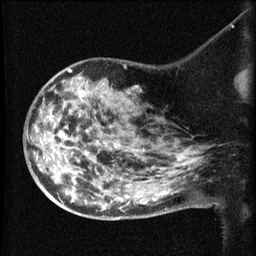
Breast MRI (dynamic contrast-enhanced), one sagittal slice; slice 40 of 60 in the series (ordered by position); dynamic contrast-enhanced series, image 2 of 3 at this slice position (ordered by acquisition); 1.5 T; TE 4.2 ms, TR 8.2 ms; 256 × 256 image matrix, field of view 180 × 180 mm. Female patient, age 50 years.
Annotated regions visible in this slice (semi-automatically segmented with operator editing):
- analysis volume of interest (the breast-tissue region the enhancement analysis was run in; not a lesion): bounding box [x1, y1, x2, y2] px = [38, 75, 169, 211]
- tumour enhancement mask (voxels above the 70 % enhancement threshold inside the analysis volume of interest): [81, 90, 85, 95]